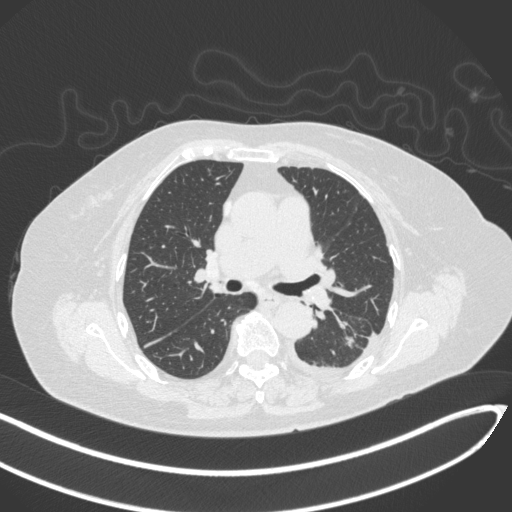
Chest CT, one axial slice; slice 188 of 270 in the series (ordered by position); lung window (W 1500 / L -600 HU); 1 mm slice thickness; 512 × 512 image matrix, field of view 400 × 400 mm. Female patient, age 76 years. From the clinical record (not read from this slice): clinical TNM (as recorded): T1c N0 M0.
Outlined on this slice (rectangle marked by the reading radiologist):
- lung tumour (recorded histology: adenocarcinoma): bounding box <343,333,358,349> (left, top, right, bottom; pixels)